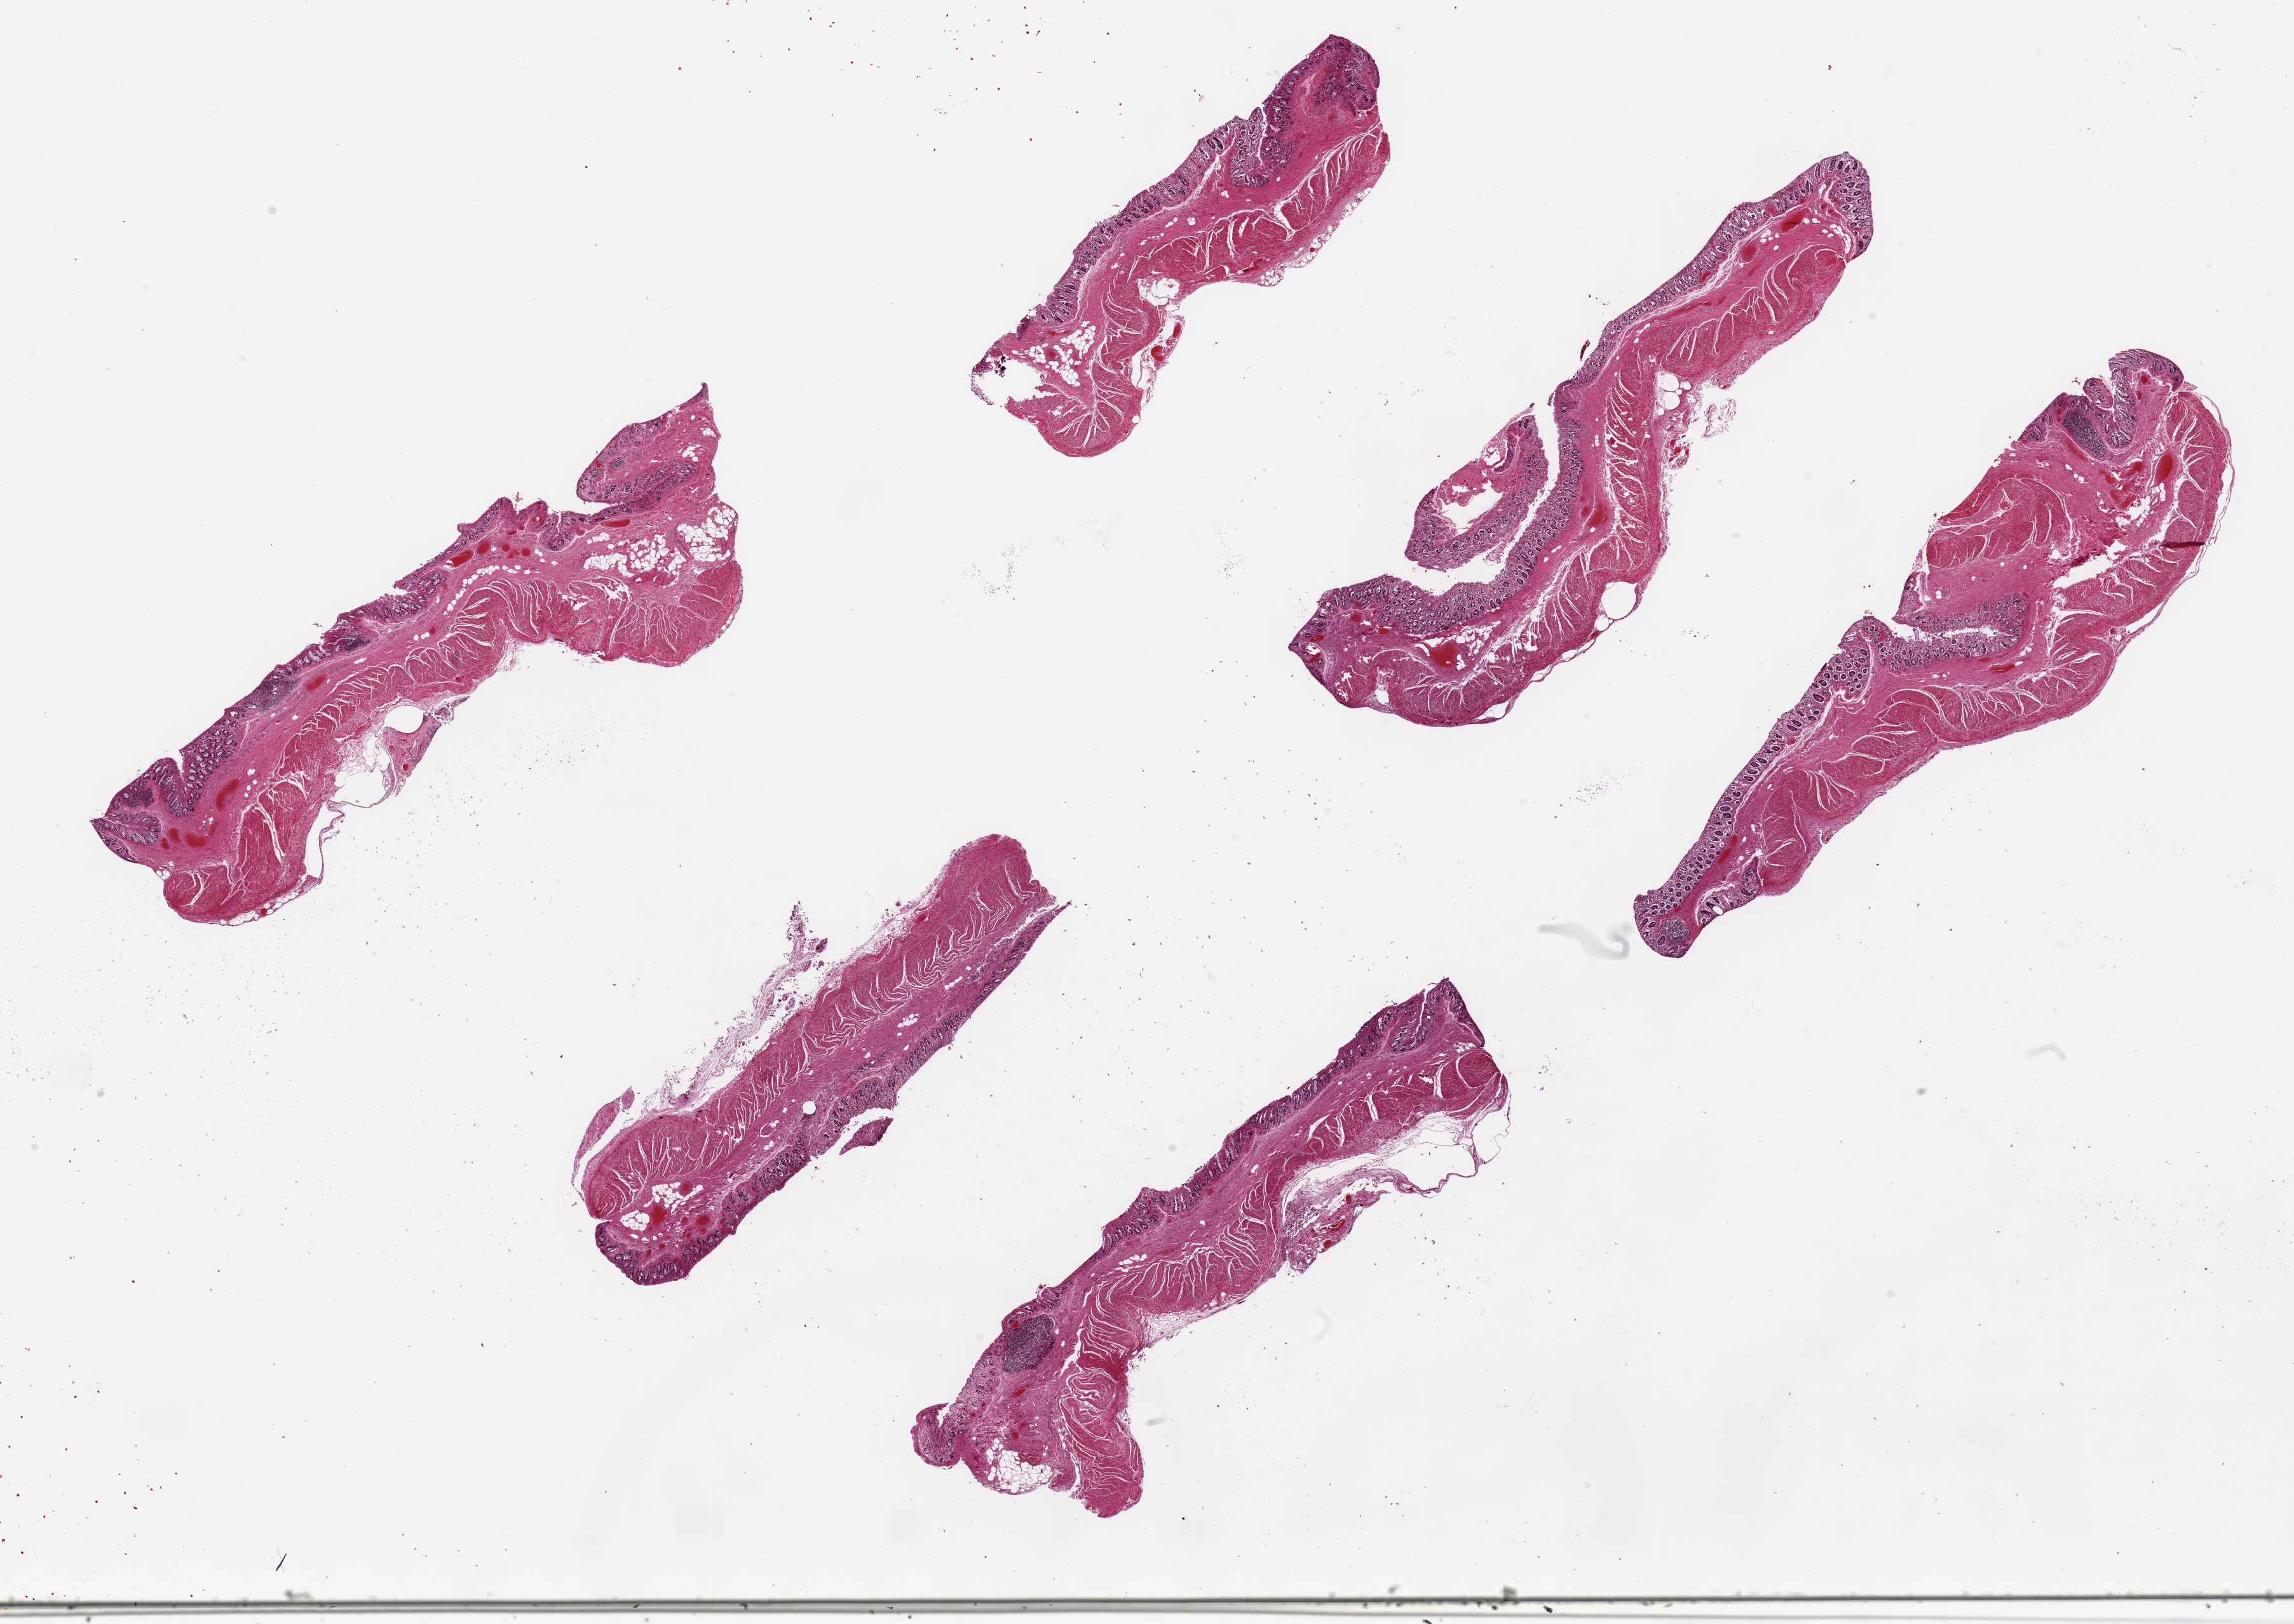
Whole-slide image, H&E stain, brightfield — low-resolution overview of the scanned area, about 28.5 x 20.2 mm (acquisition: 20x scan); PAXgene-fixed, paraffin-embedded tissue; target tissue: transverse colon; tissue donor sample.
Pathologist's review note for this sample: 6 pieces, ~7x1.5. Mucosal glands badly autolyzed, ~15-20% of thickness.